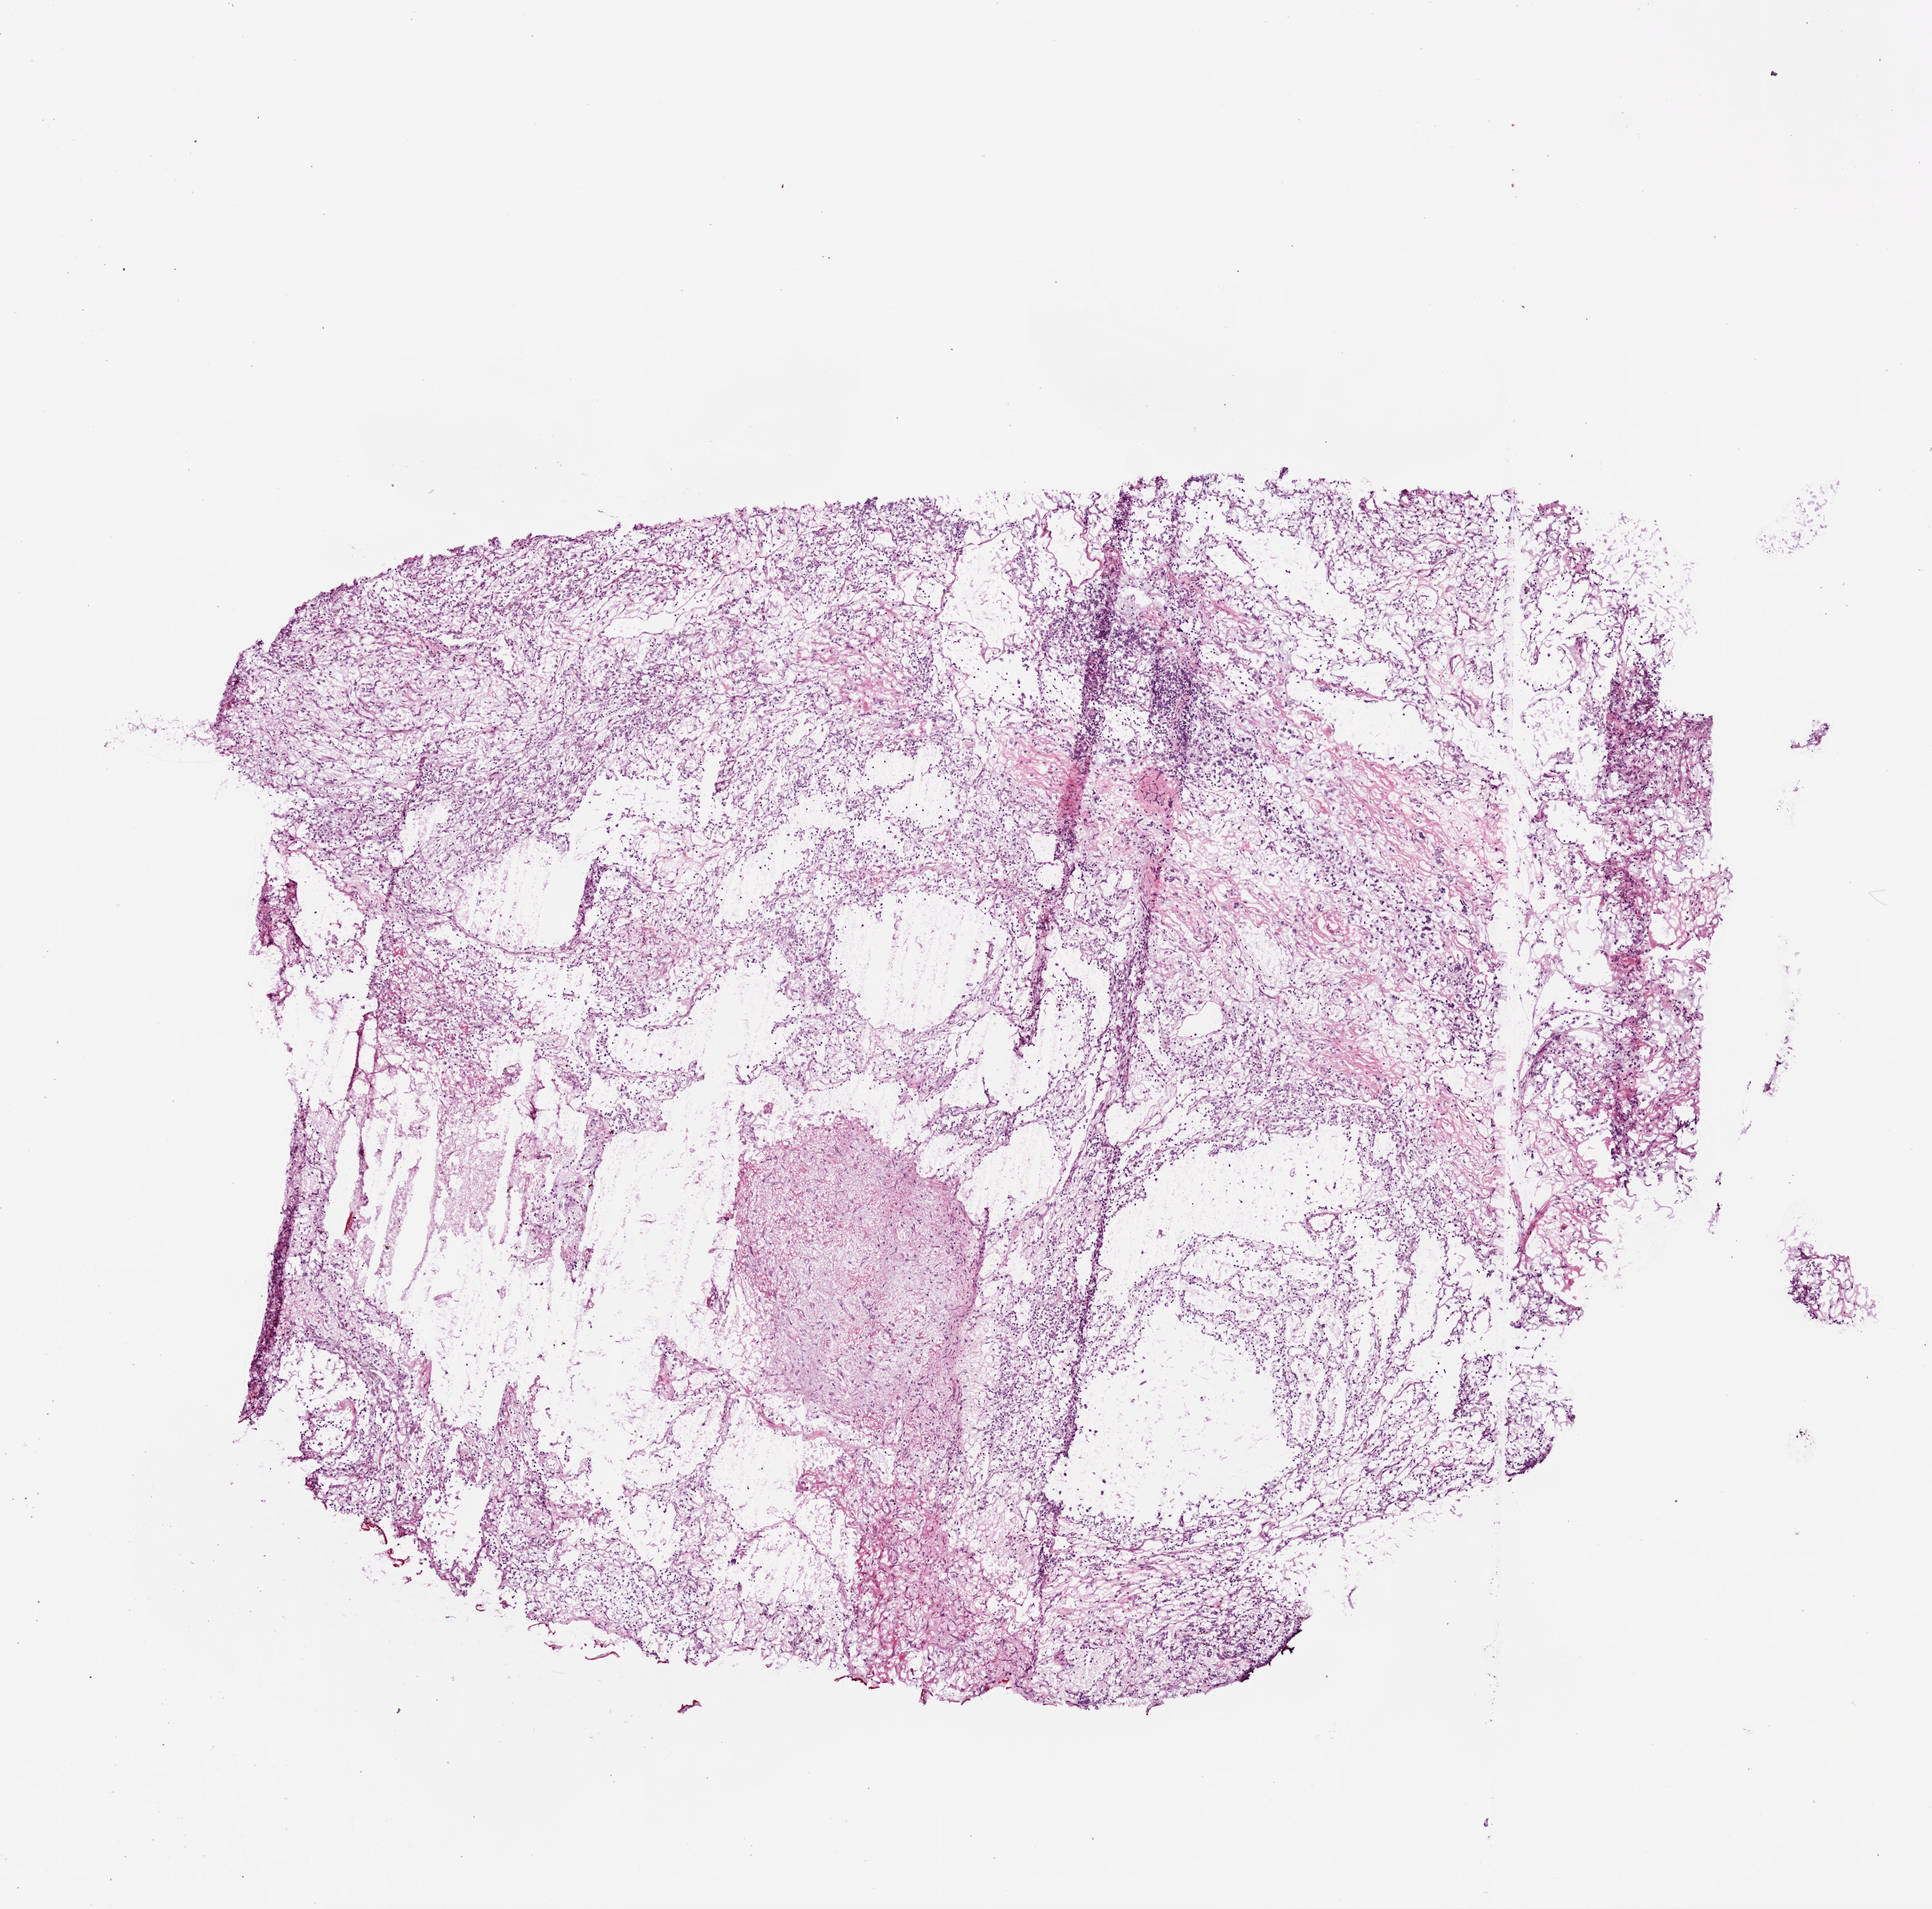
Digitized H&E tissue section (whole slide) — low-resolution overview of the scanned area, about 6.0 x 5.9 mm (slide scanned at 20x). Frozen section. Kidney, primary tumour sample. Patient: male, age at initial diagnosis 62 years. Histologic grade: G2 (moderately differentiated). Composition of this section per pathologist review: tumour cells 90%, tumour nuclei 75%, normal cells 0%, stromal cells 10%, necrosis 0%.
TNM: T2a NX M0. AJCC pathologic stage: II (7th edition). Diagnosis: Clear cell adenocarcinoma, NOS.